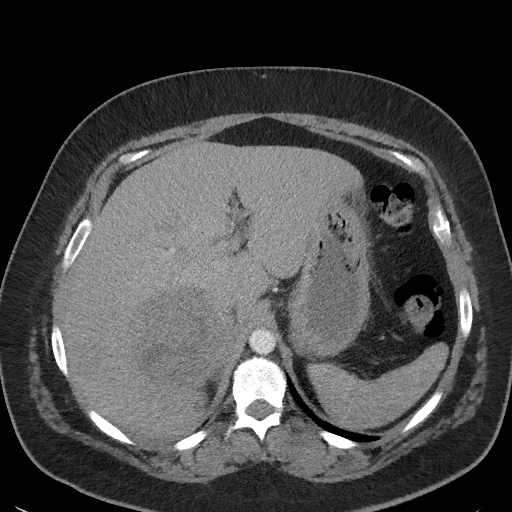
Contrast-enhanced abdominal CT, one axial slice; position 39 of 56 along the scan axis; reconstruction kernel I41f/3; intravenous contrast given; soft-tissue window (W 400 / L 40 HU); 5 mm slice thickness; 512 × 512 image matrix, field of view 373 × 373 mm. Female patient, age 35 years. Case-level facts recorded for this patient, not image findings: diagnosis: adrenocortical carcinoma; tumour side: right adrenal; tumour size at pathology: 15 cm; Ki-67 index: 40 %; stage (as recorded): 2.
Outlined on this slice (semi-automatically segmented with operator editing):
- mass: box from (x=133, y=291) to (x=225, y=383) px